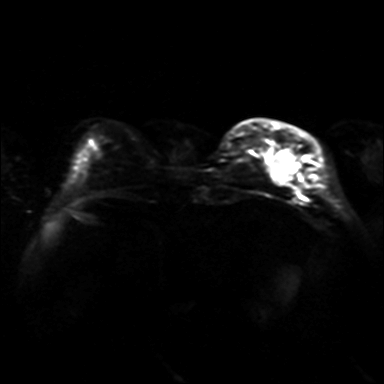
Breast MRI, one axial slice. Position 8 of 36 along the scan axis. Diffusion-weighted series; image 2 of 4 stored at this slice position (different b-values; order by instance number). 3 T. 4 mm slice thickness. 384 × 384 image matrix, field of view 320 × 320 mm. Female patient.
Outlined on this slice (expert manual segmentation):
- tumour on diffusion-weighted imaging: bounding box <271,152,299,183> (left, top, right, bottom; pixels)